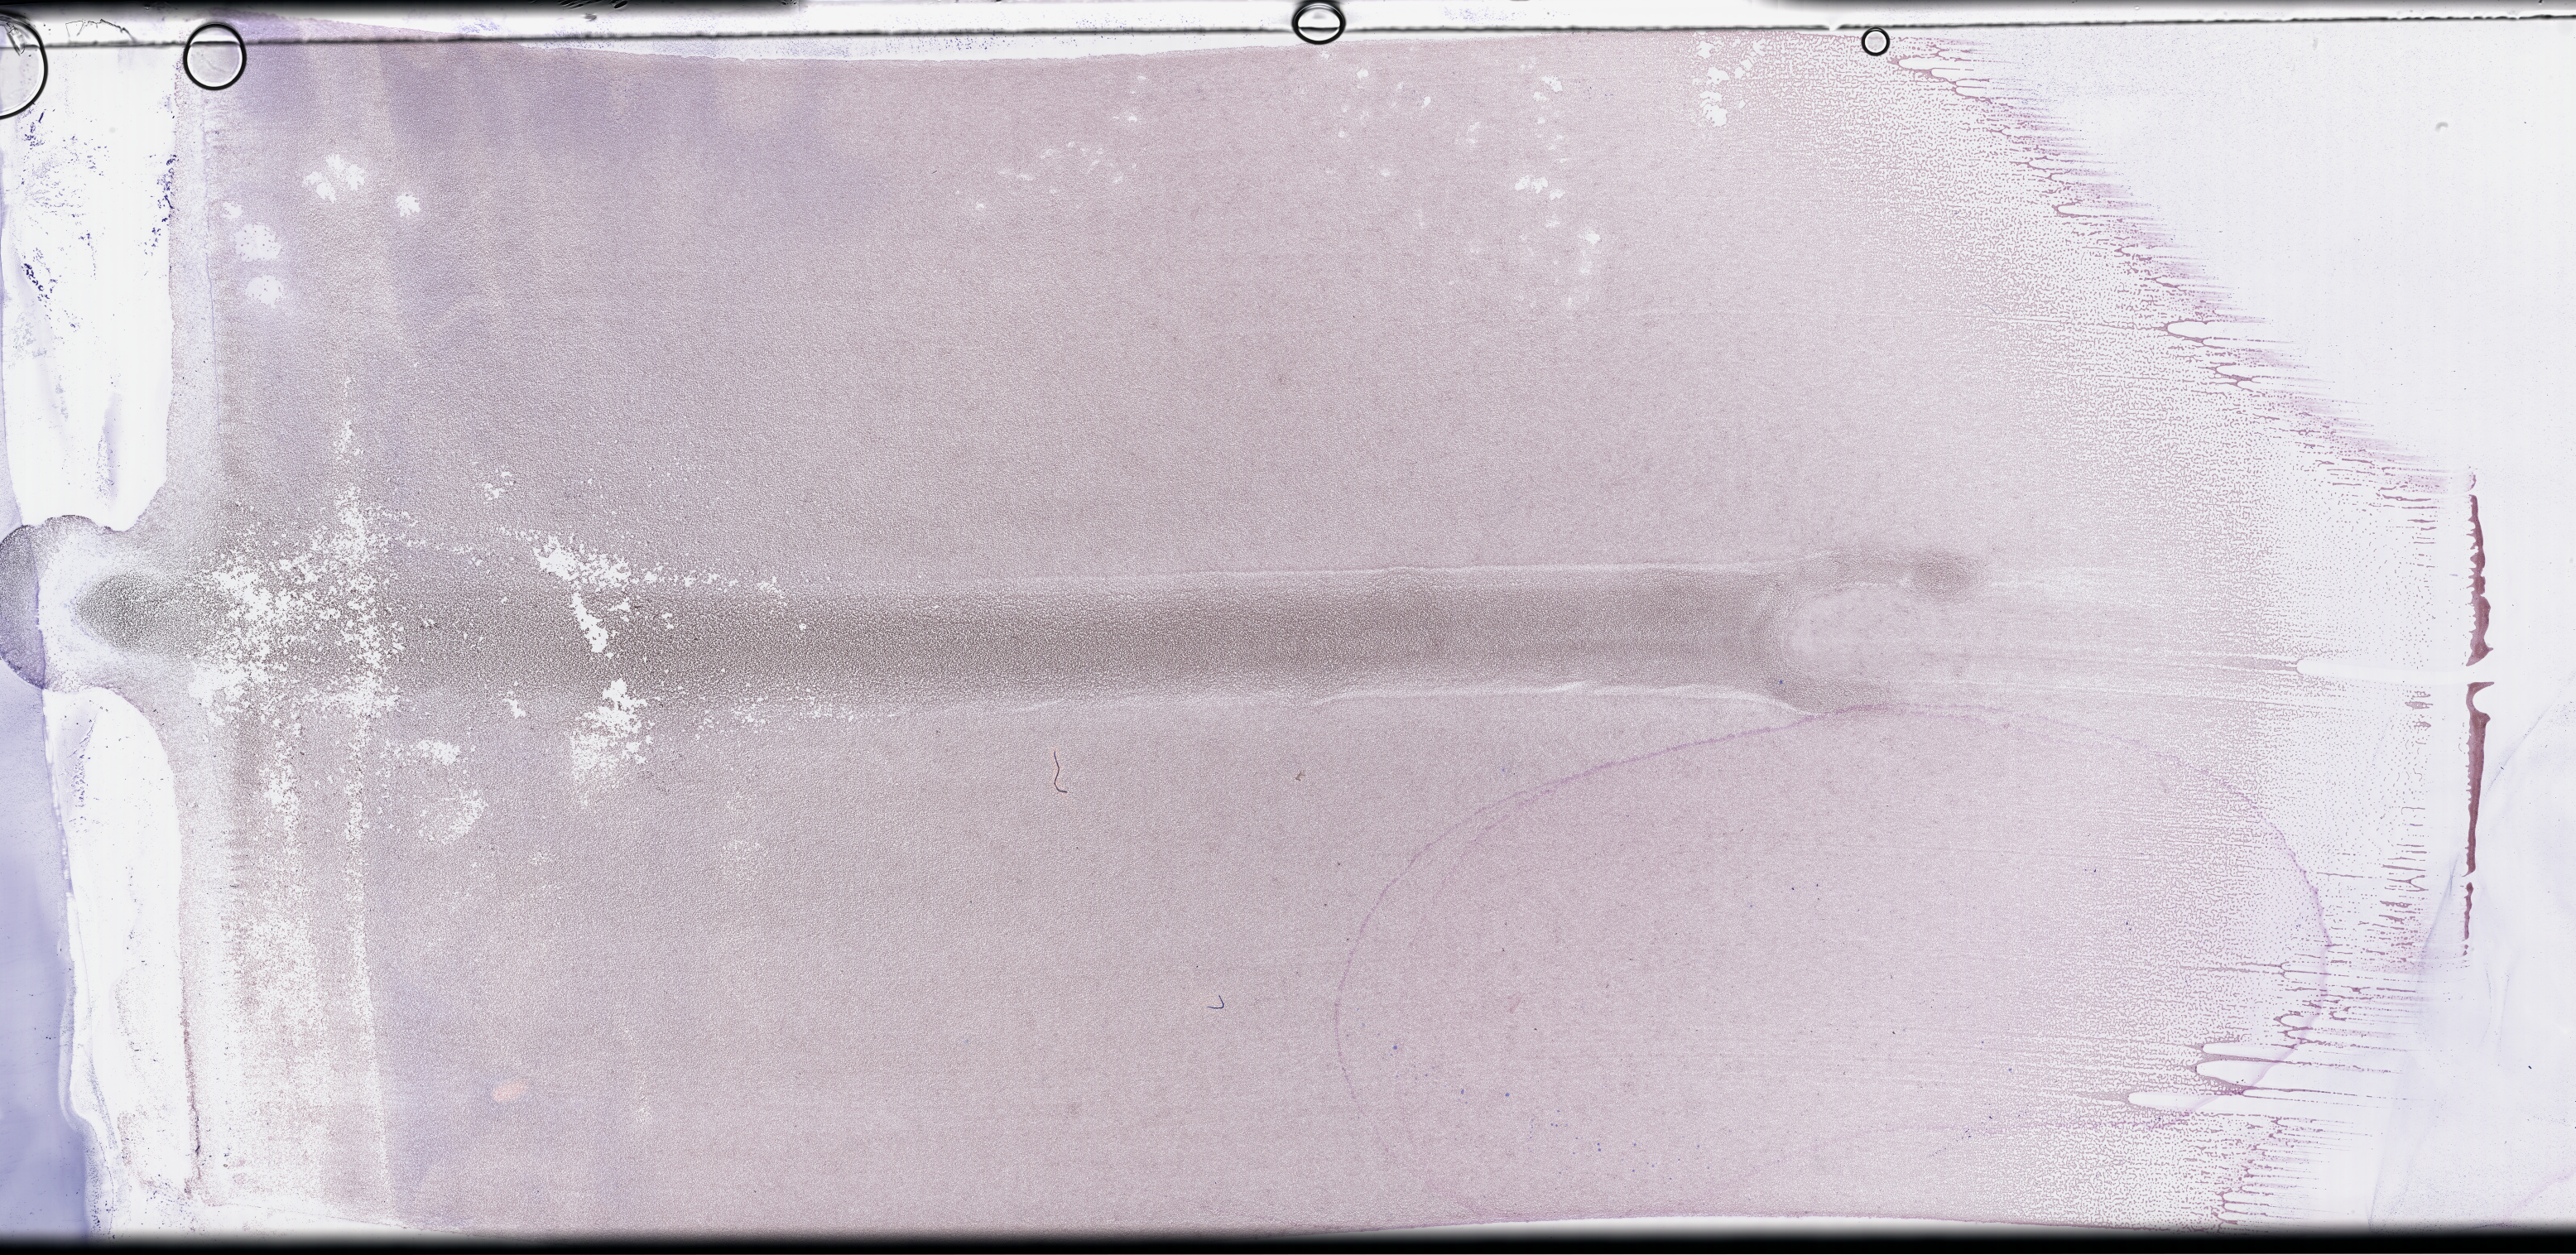
Whole-slide image of a whole blood smear, Wright-Giemsa stain, shown as a low-resolution overview of the whole scanned area (about 50.3 x 24.5 mm), specimen time point: collected at baseline (before treatment). Female patient.
- from a patient with: Plasma Cell Myeloma